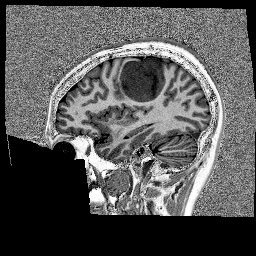
Brain MRI from a brain-tumour surgery series, one sagittal slice; position 54 of 176 along the scan axis; 1 mm slice thickness; 256 × 256 image matrix. Case-level facts recorded for this patient, not image findings: histopathology: Glioblastoma; WHO grade: 4; IDH mutation: no.
Annotated regions visible in this slice (manually delineated by an expert):
- tumour: bounding box (x1, y1, x2, y2) in pixels: (118, 58, 175, 105)